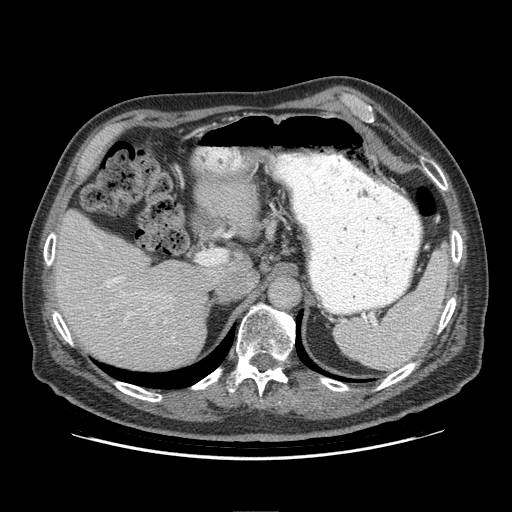
Contrast-enhanced abdominal CT (liver protocol), one axial slice; position 61 of 95 along the scan axis; soft-tissue window (W 400 / L 40 HU); 2.5 mm slice thickness; 512 × 512 image matrix. From the clinical record (not read from this slice): diagnosis: hepatocellular carcinoma (patient treated with transarterial chemoembolisation; whether this scan precedes or follows treatment is not stated here); TNM stage (as recorded): Stage-IVB; Child-Pugh class: A.
Structures marked on this image (semi-automatically segmented with operator editing):
- liver parenchyma outside the tumour (the mass and vessels are separate outlines, so this box may not span the whole liver): box from (x=54, y=210) to (x=246, y=370) px
- liver vessels: (x=107, y=277)–(x=119, y=288)